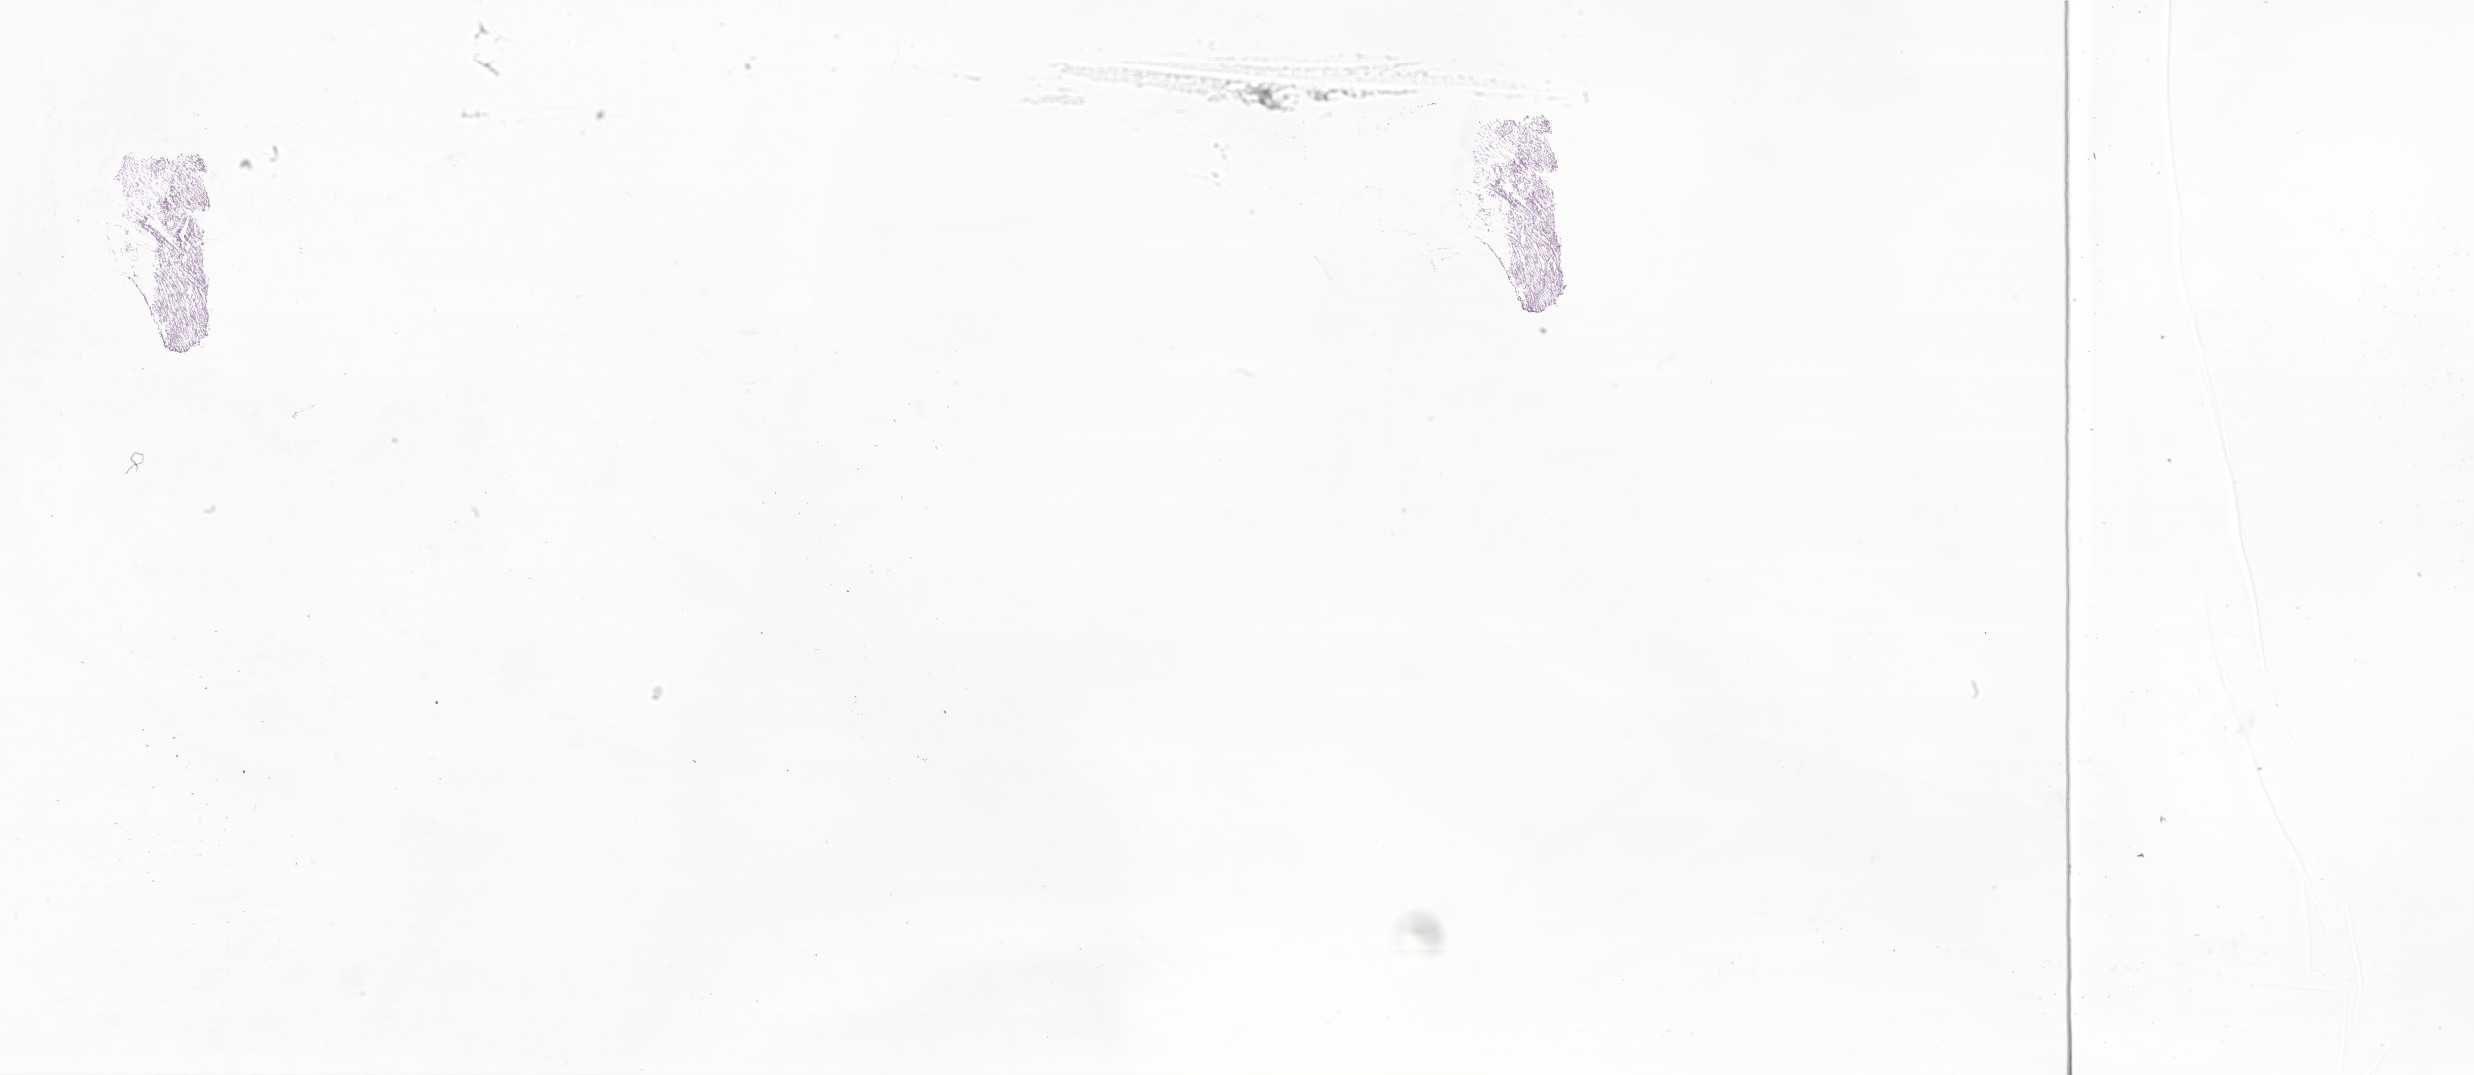
Whole-slide image, hematoxylin and eosin (H&E) stain of tumor tissue from the frontal lobe, a low-resolution overview of the entire scanned area, about 41.7 x 18.1 mm. Frozen section. Female patient, age 412 days (about 1.1 years).
Recorded diagnosis: Neoplasm, uncertain whether benign or malignant.